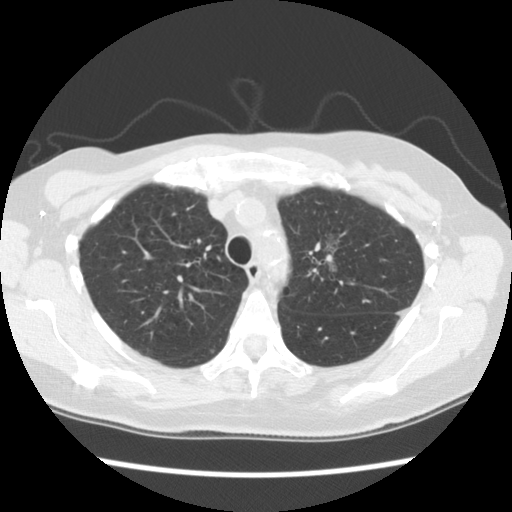
Axial slice from a low-dose chest CT screening exam; second annual screen; lung window (W 1500 / L -600 HU); 2.5 mm slice thickness; standard (soft-tissue) reconstruction kernel (STANDARD); slice 80 of 110 in the series; 512 × 512 image matrix. Female, age 65 years at enrolment. Former smoker at enrolment.
• Expert-annotated lung lesion, bounding box [x1, y1, x2, y2] px = [301, 223, 363, 286].
• The screening reader recorded 2 non-calcified nodules or masses ≥4 mm on this exam (right upper lobe, left upper lobe); which of them this box marks is not recorded.
• Official screen result: positive, other.
• Lung cancer was diagnosed 481 days after this screen: adenocarcinoma, NOS, left upper lobe, moderately differentiated (G2), stage IA (AJCC 6th edition), 30 mm at pathology.